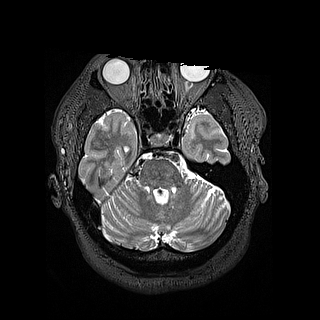
Brain MRI from a brain-tumour surgery series, one axial slice; slice 108 of 144 in the series (ordered by position); 1.2 mm slice thickness; 320 × 320 image matrix, field of view 254 × 254 mm. Case-level facts recorded for this patient, not image findings: histopathology: Astrocytoma; WHO grade: 2; IDH mutation: yes; tumour location: Left Insular.
Annotated regions visible in this slice (expert manual segmentation):
- tumour: bounding box [x1, y1, x2, y2] px = [188, 127, 196, 140]